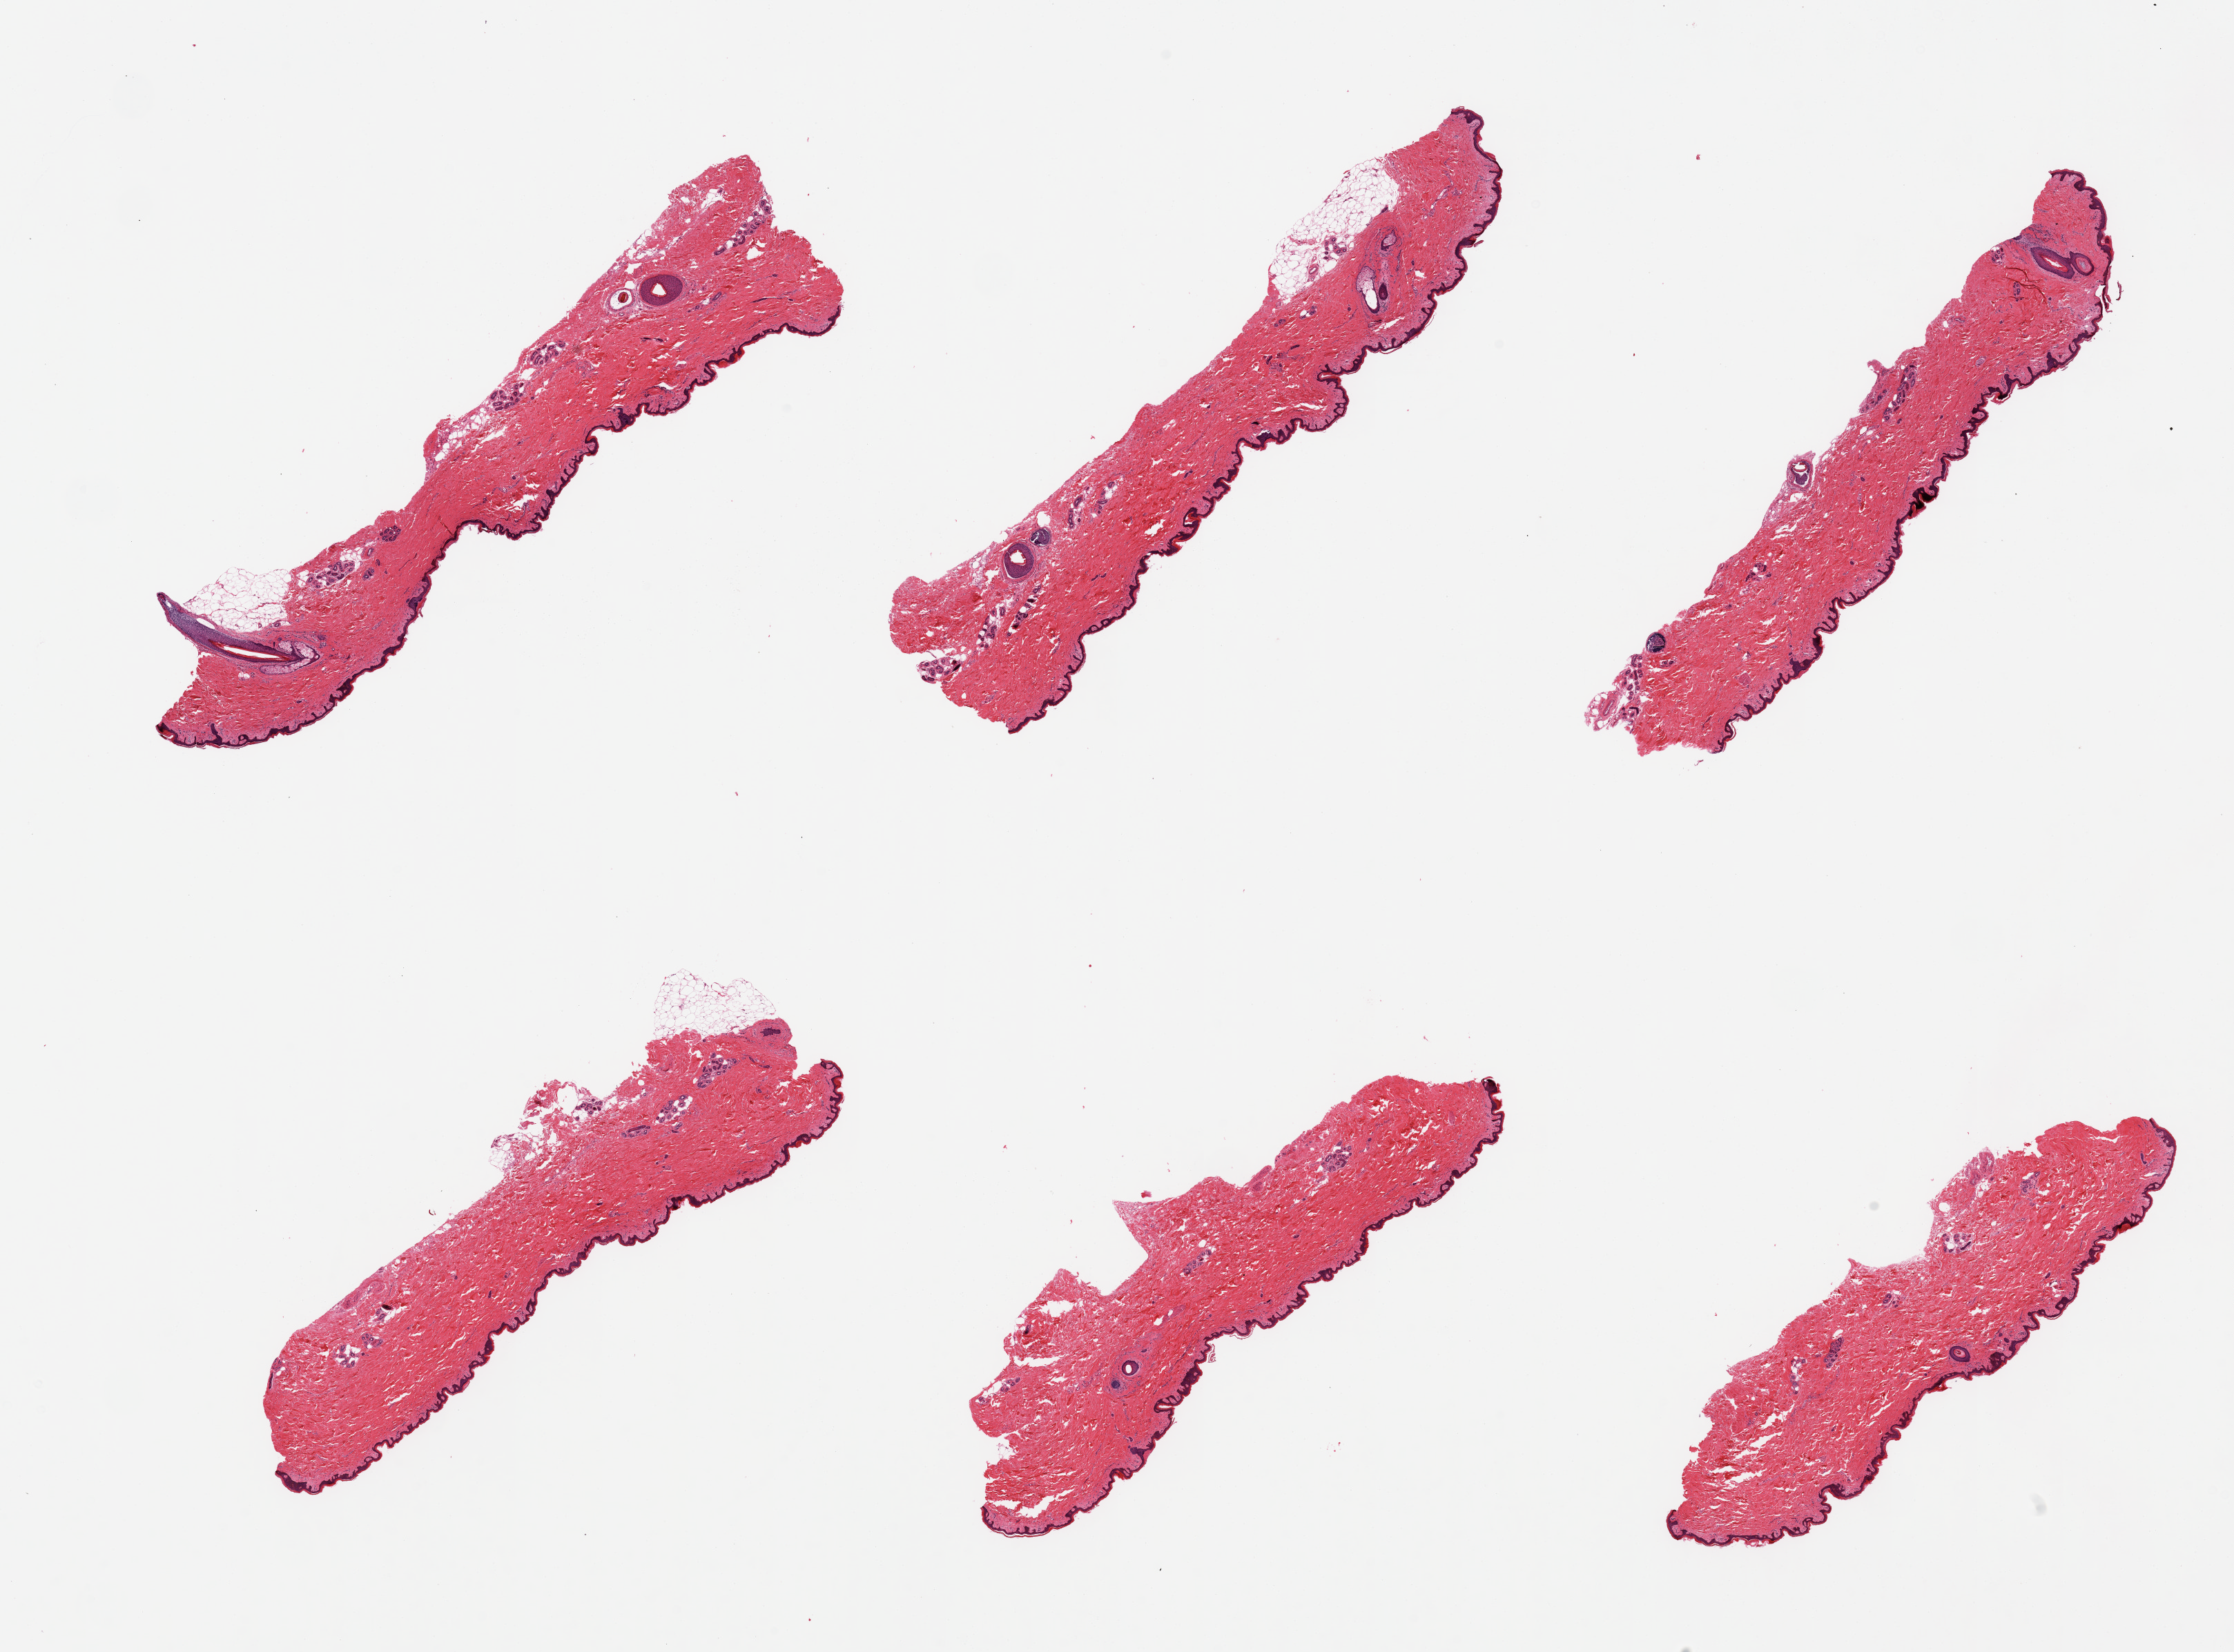
Whole-slide image, H&E stain — a low-resolution overview of the entire scanned area, about 25.6 x 18.9 mm; PAXgene-fixed, paraffin-embedded tissue; section of skin of suprapubic region (target tissue); donor tissue sample. Donor sex: female.
Review note (as recorded): 6 pieces, no dermalt fat; squamous epithelium is ~30-50 microns.